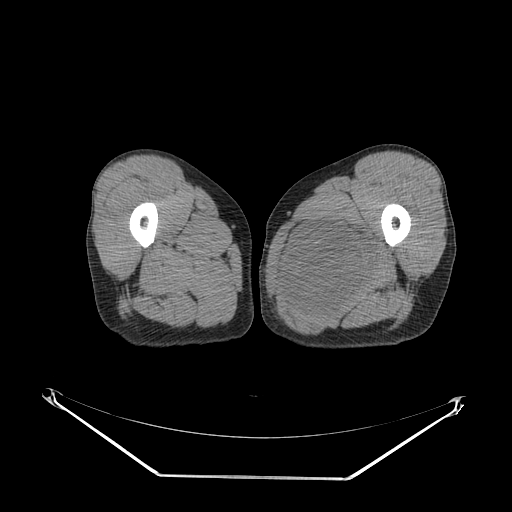
CT of an extremity soft-tissue mass (from a PET/CT study), one axial slice. Position 26 of 267 along the scan axis. Reconstruction kernel SOFT. Soft-tissue window (W 400 / L 40 HU). 3.75 mm slice thickness. 512 × 512 image matrix, field of view 500 × 500 mm. Male patient. Case-level facts recorded for this patient, not image findings: histological type: pleiomorphic liposarcoma; grade: high; site of the primary tumour: left thigh.
Annotated regions visible in this slice (expert contour drawn on MRI and transferred to this co-registered scan by the dataset authors):
- gross tumour volume including surrounding oedema: bounding box [x1, y1, x2, y2] px = [285, 217, 385, 314]
- gross tumour volume (mass): [290, 221, 373, 309]